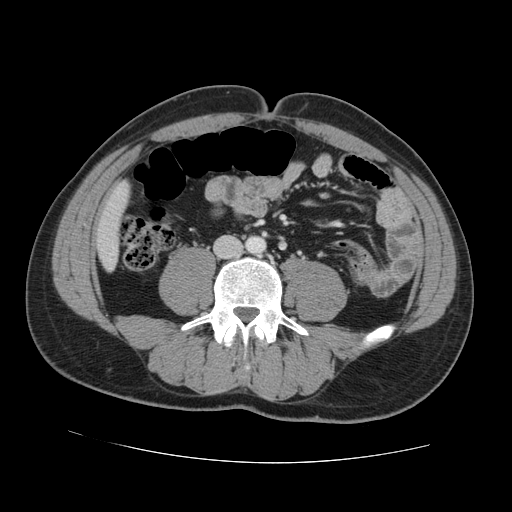
Contrast-enhanced abdominal CT, one axial slice. Slice 13 of 131 in the series (ordered by position). Intravenous contrast given. Soft-tissue window (W 400 / L 40 HU). 512 × 512 image matrix. Male patient, age 40 years. From the clinical record (not read from this slice): diagnosis: colorectal cancer liver metastases, imaged before liver resection; multiple liver metastases: yes; largest metastasis: 2.9 cm; disease in both lobes: yes.
Outlined on this slice (outlined manually by an expert reader):
- liver: bounding box (x1, y1, x2, y2) in pixels: (98, 187, 129, 268)